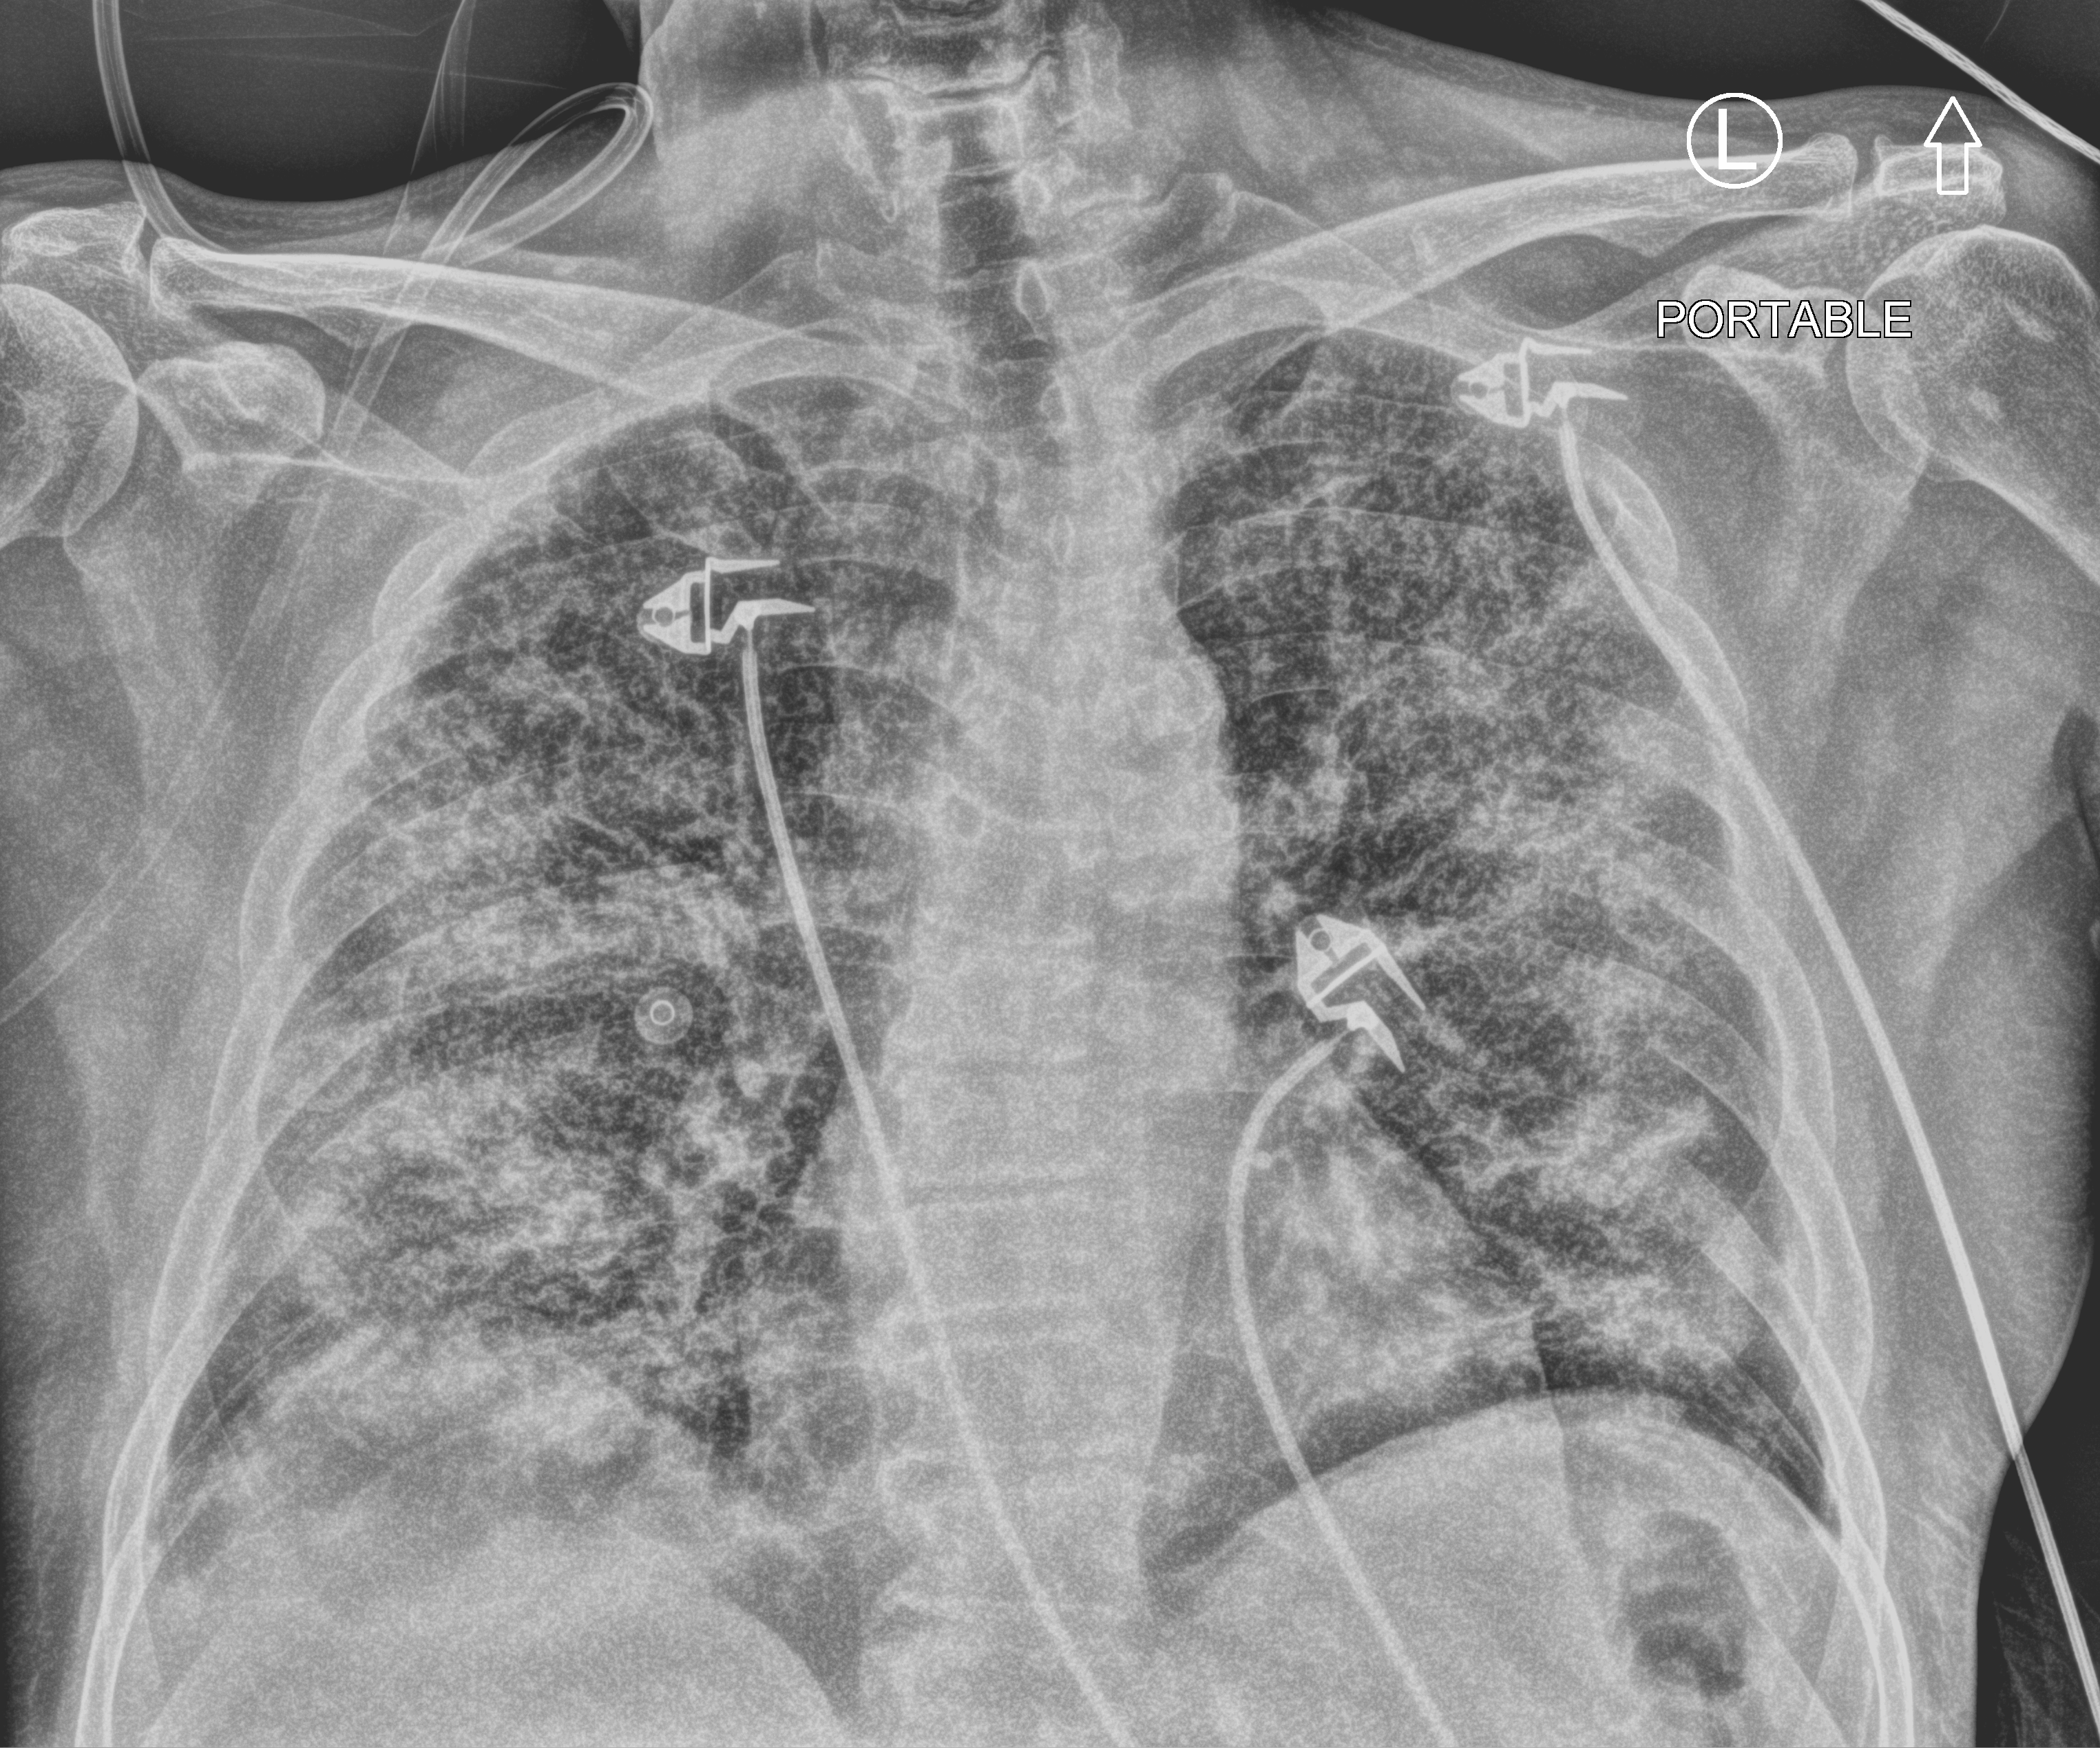
Bedside chest radiograph (computed radiography), anteroposterior (AP) projection. Male patient hospitalised with COVID-19, age 18–59 years.
Hospital-stay facts (about this admission, not read from this image; timing relative to this image not recorded): mechanically ventilated during this hospital stay: no.